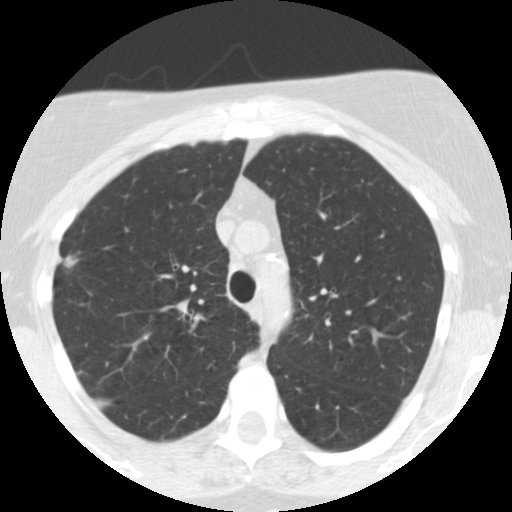
Chest CT (low-dose screening protocol), one axial image, third screening round (two years after baseline), lung window (W 1500 / L -600 HU), 2.5 mm slice thickness, slice 184 of 248 in the series. Female participant, aged 55 years at enrolment. Current smoker at enrolment.
• Lesion marked by an expert reader, bounding box <49,240,93,282> (left, top, right, bottom; pixels).
• Screening reader's record for this exam (one nodule recorded; not confirmed to be the boxed lesion): non-calcified nodule or mass ≥4 mm, right upper lobe, 10 × 10 mm, poorly defined margins, soft tissue attenuation, pre-existing on the prior screen: yes; interval growth: yes.
• Official screen result: positive, other.
• Lung cancer was diagnosed 145 days after this screen: bronchiolo-alveolar adenocarcinoma, NOS, right upper lobe, moderately differentiated (G2), stage IIA (AJCC 6th edition), 13 mm at pathology.